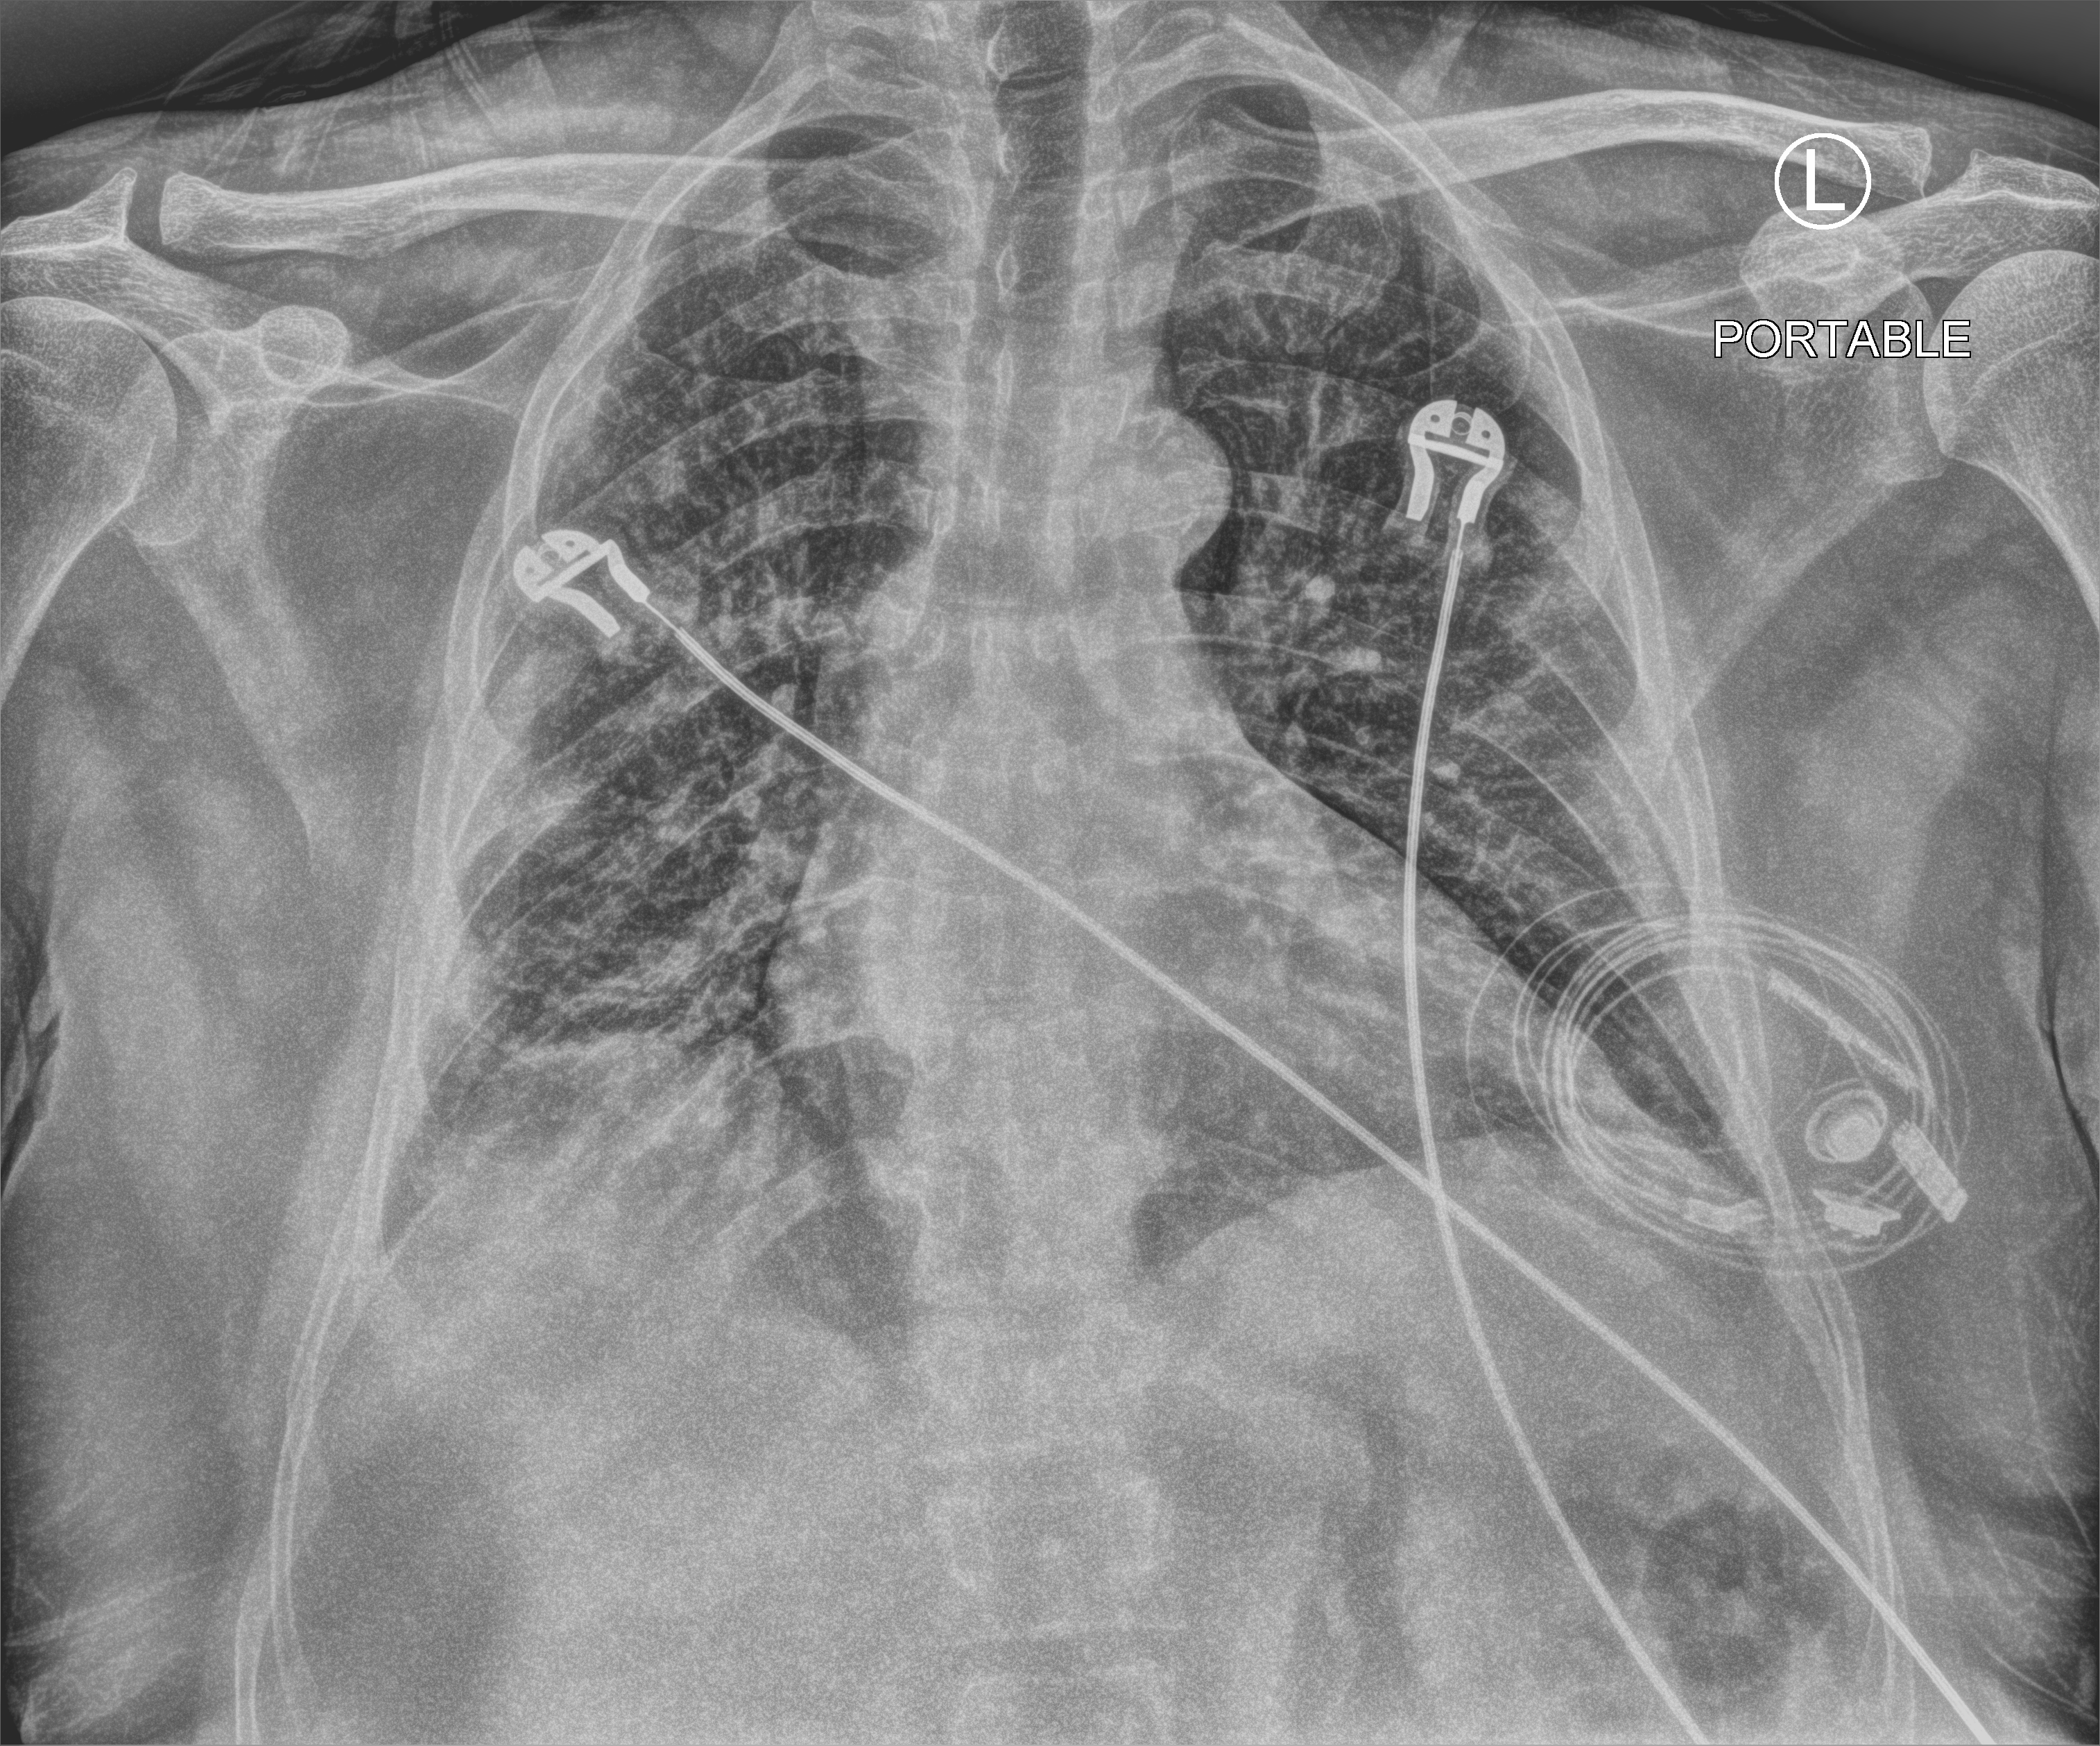
Portable chest radiograph, anteroposterior (AP) projection. Male patient hospitalised with COVID-19, age 60–74 years.
Hospital-stay facts (about this admission, not read from this image; timing relative to this image not recorded): admitted to intensive care during this hospital stay: yes; smoking status (admission record): never.